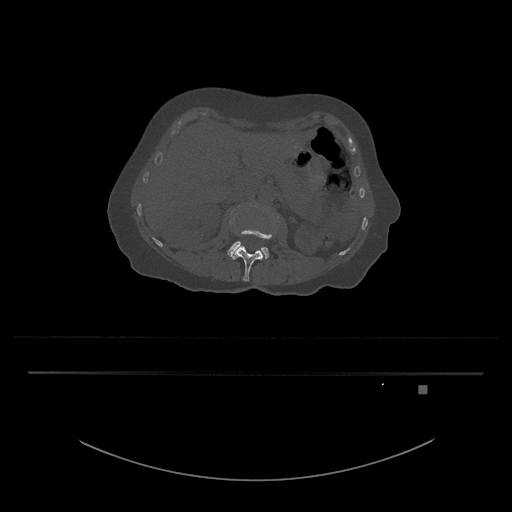
CT including the spine, one axial slice; position 471 of 797 along the scan axis; reconstruction kernel Br40s/3; bone window (W 1800 / L 400 HU); 0.5 mm slice thickness; 512 × 512 image matrix. Patient: female, 57 years. Case-level facts recorded for this patient, not image findings: primary cancer: cervical.
Structures marked on this image (semi-automatic segmentation, software-assisted and operator-edited):
- L3 vertebra: bounding box (x1, y1, x2, y2) in pixels: (227, 205, 269, 259)